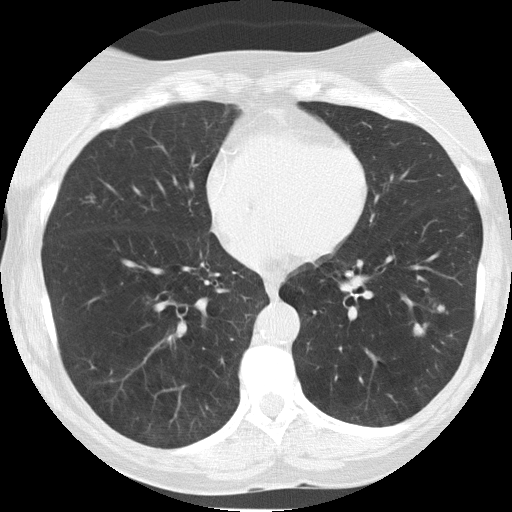
Low-dose screening chest CT, one axial slice. Slice 63 of 149 in the series (ordered by position). Reconstruction kernel FC51. 120 kVp. Lung window (W 1500 / L -600 HU). 512 × 512 image matrix, field of view 290 × 290 mm.
Outlined on this slice (expert manual segmentation):
- lesion 1 (tumor, lower lobe of left lung): bounding box [x1, y1, x2, y2] px = [414, 305, 445, 335]